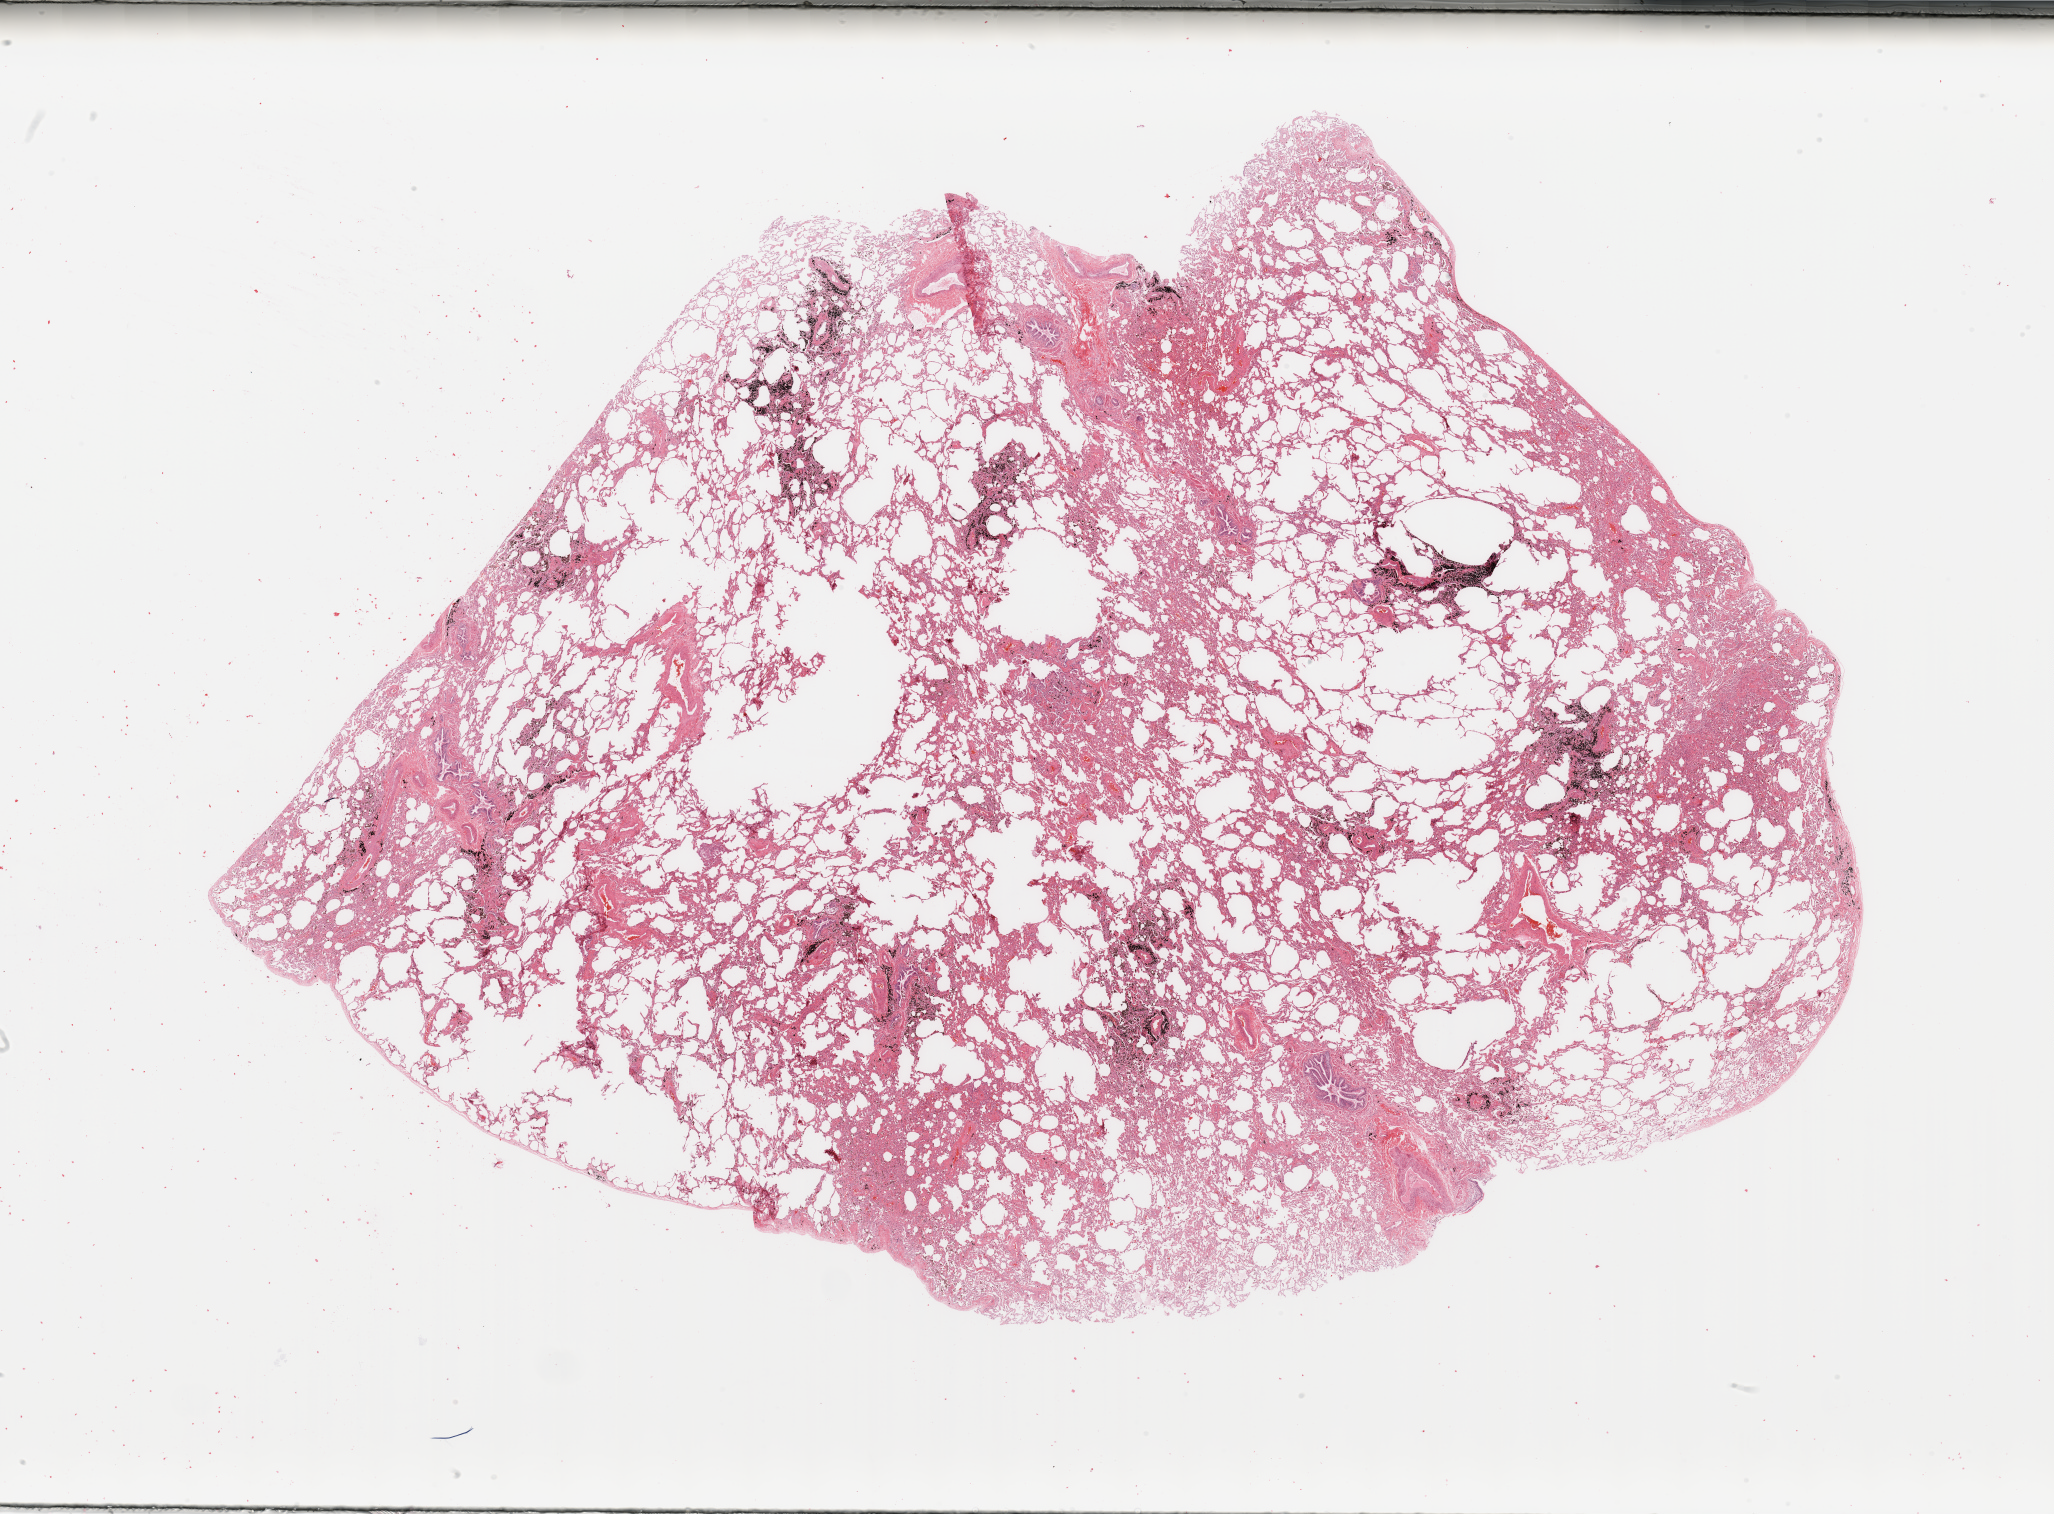
Digitized H&E tissue section (whole slide) — low-resolution overview of the scanned area, about 32.5 x 23.9 mm (from a 20x scan); normal (non-tumour) tissue sample, sampled site: lung. Male, 55 y/o.
- this section: normal (non-tumour) tissue from the same patient
- patient diagnosis: Adenocarcinoma, NOS